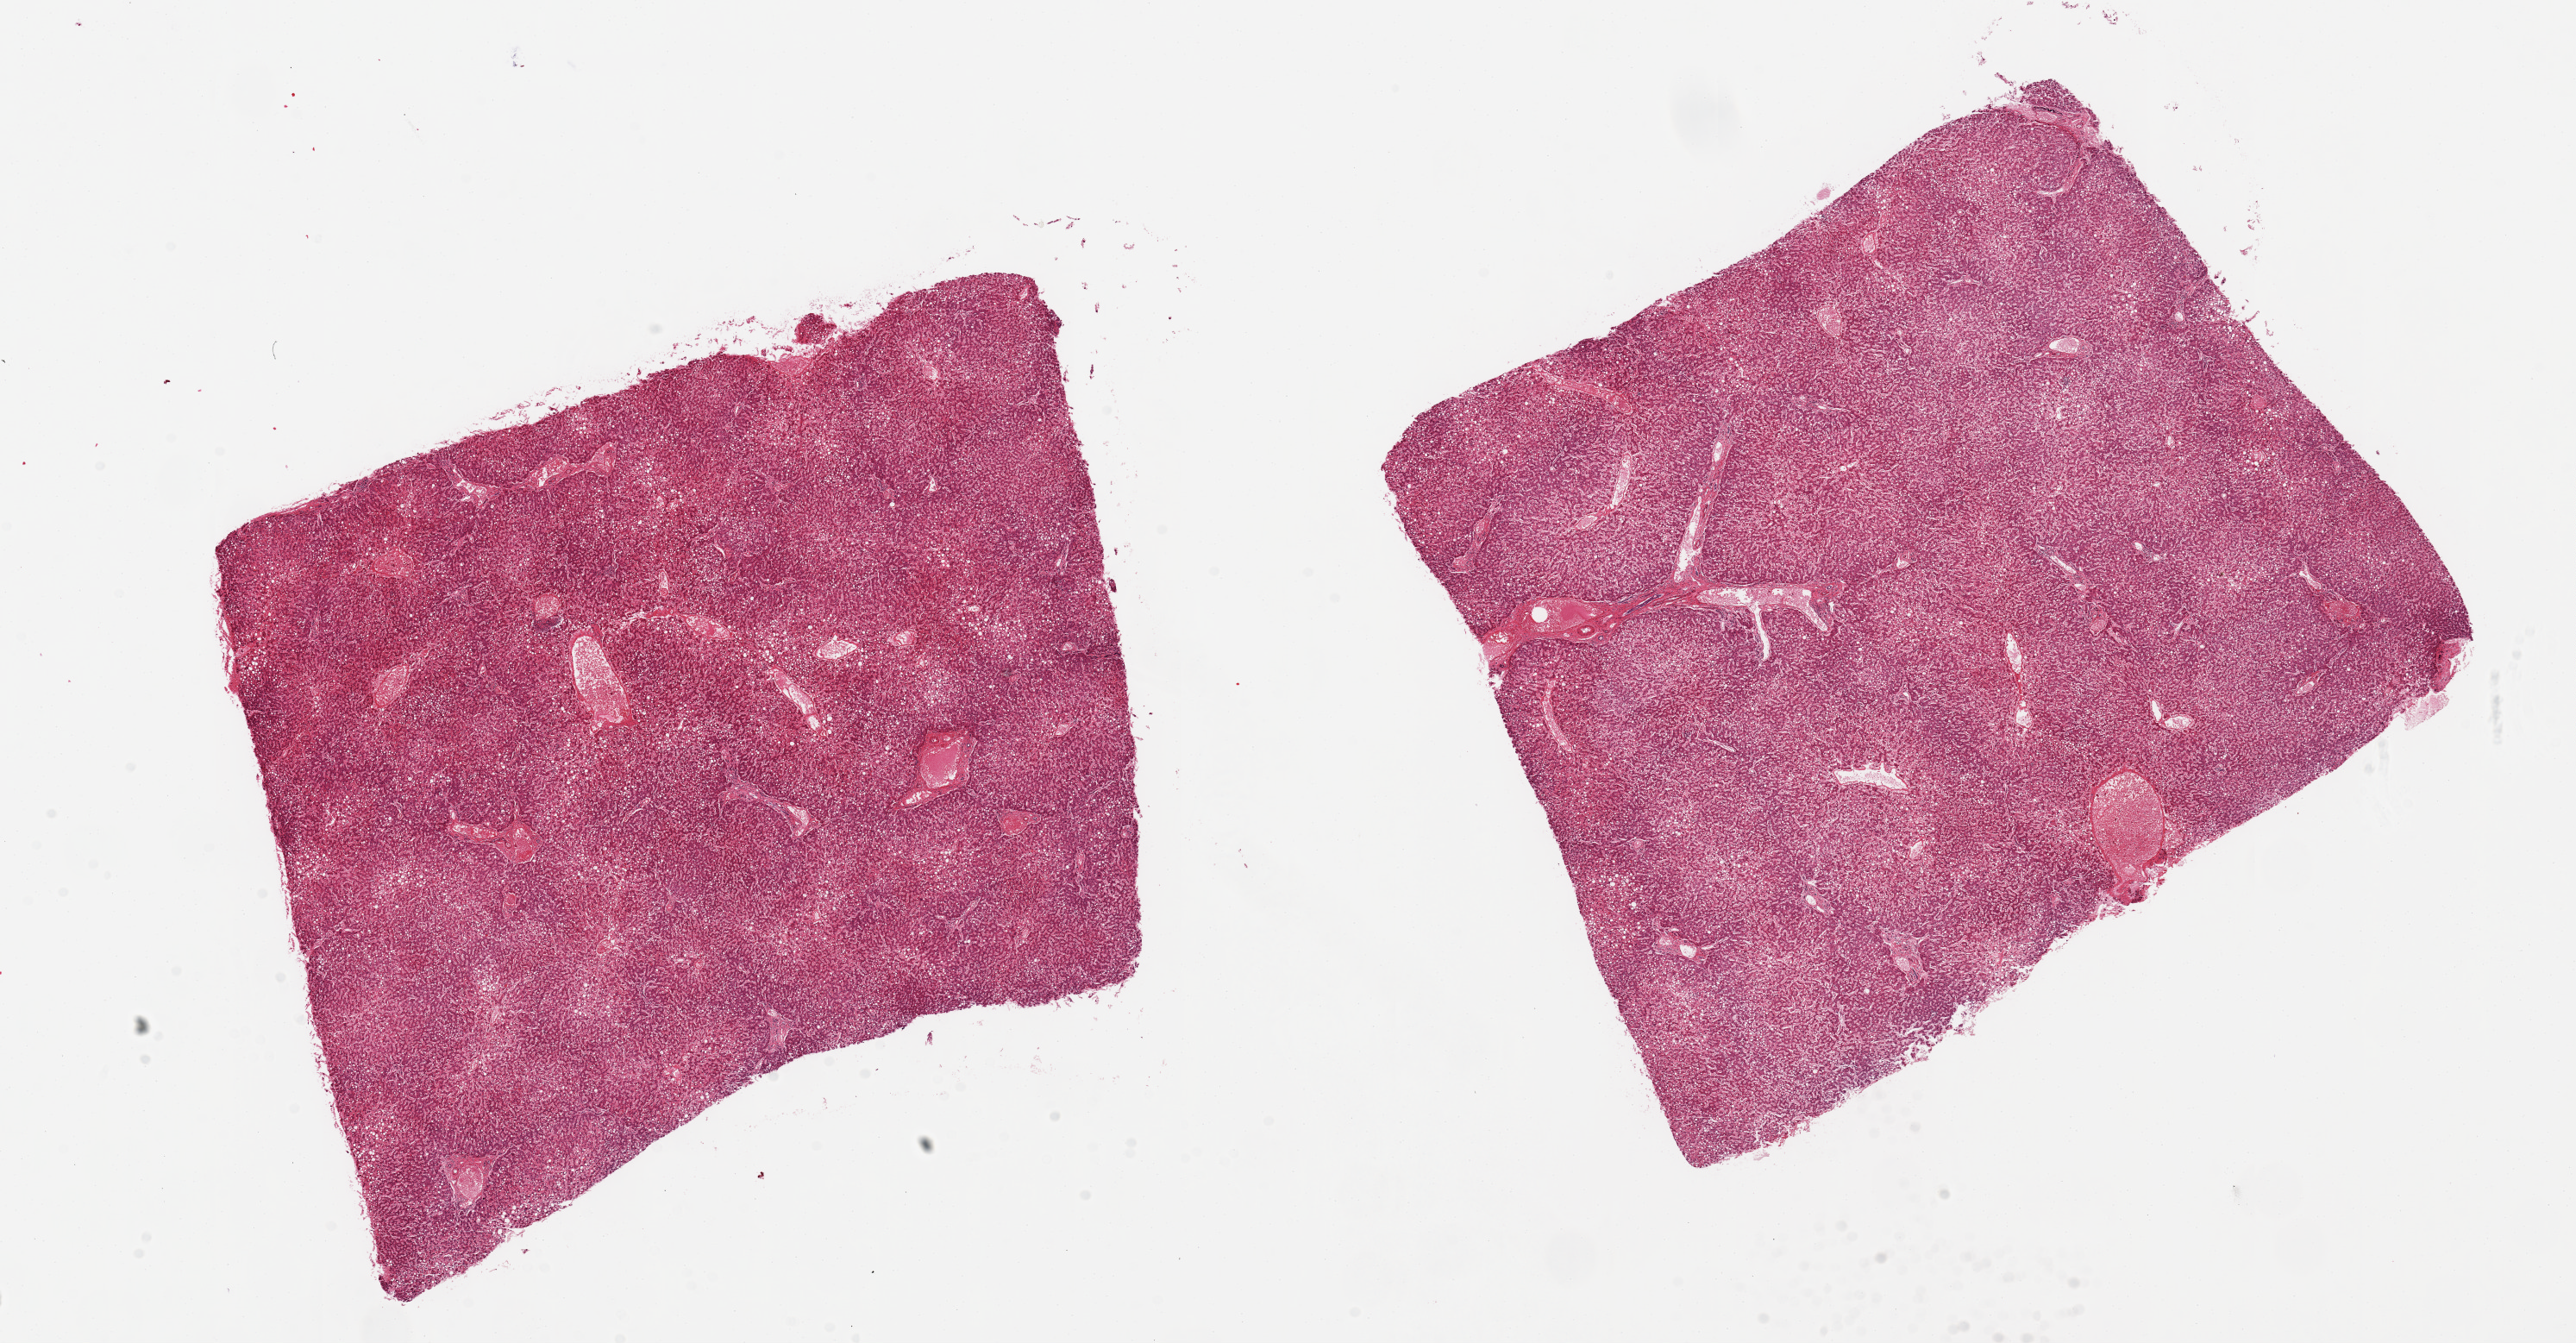
Digitized haematoxylin and eosin-stained section — shown as a low-resolution overview of the whole scanned area (about 23.6 x 12.3 mm). PAXgene-fixed paraffin-embedded (PFPE) section. Sampled site (target tissue): liver. Tissue donor sample. Male donor.
Pathologist's review note for this sample: 2 pieces ~8x7mm, diffuse macro and micro vesicular steatosis.